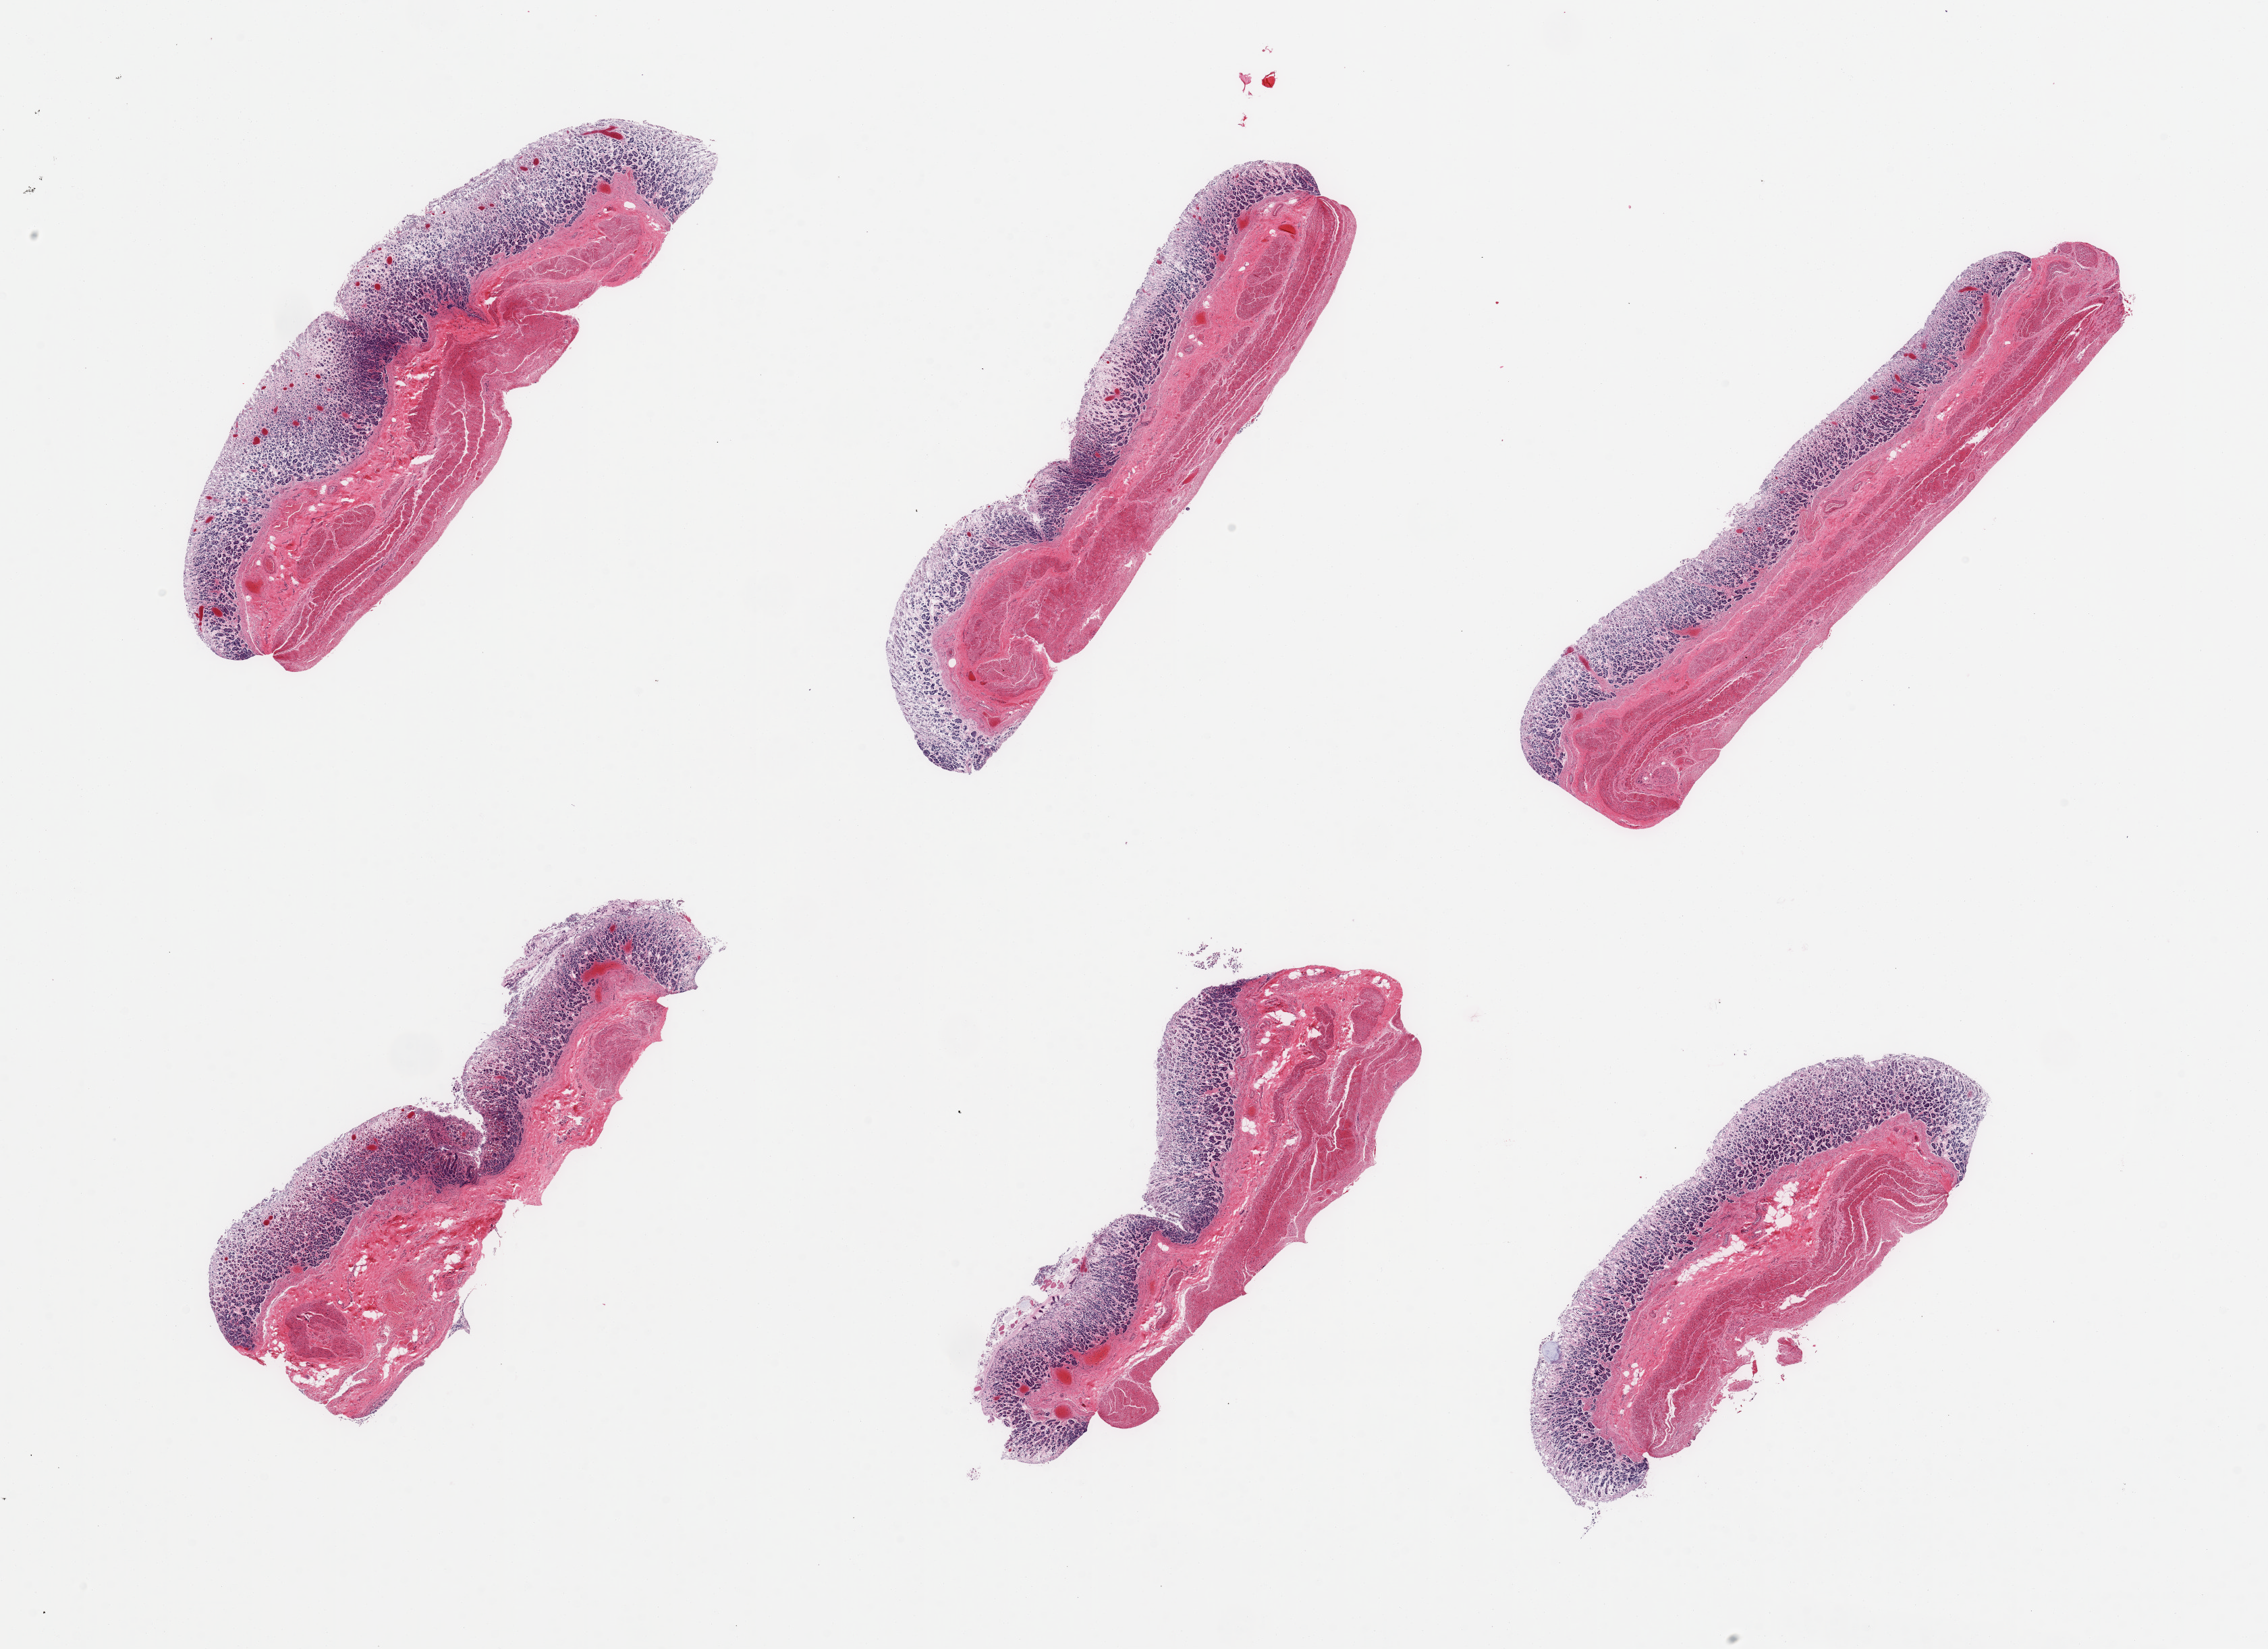
Hematoxylin and eosin (H&E) whole-slide image, brightfield — shown as a low-resolution overview of the whole scanned area (about 26.6 x 19.3 mm, slide scanned at 20x); PAXgene-fixed, paraffin-embedded tissue; sampled site (target tissue): stomach; tissue donor sample.
- pathologist's review note for this sample: 6 pieces; mucosa and muscularis